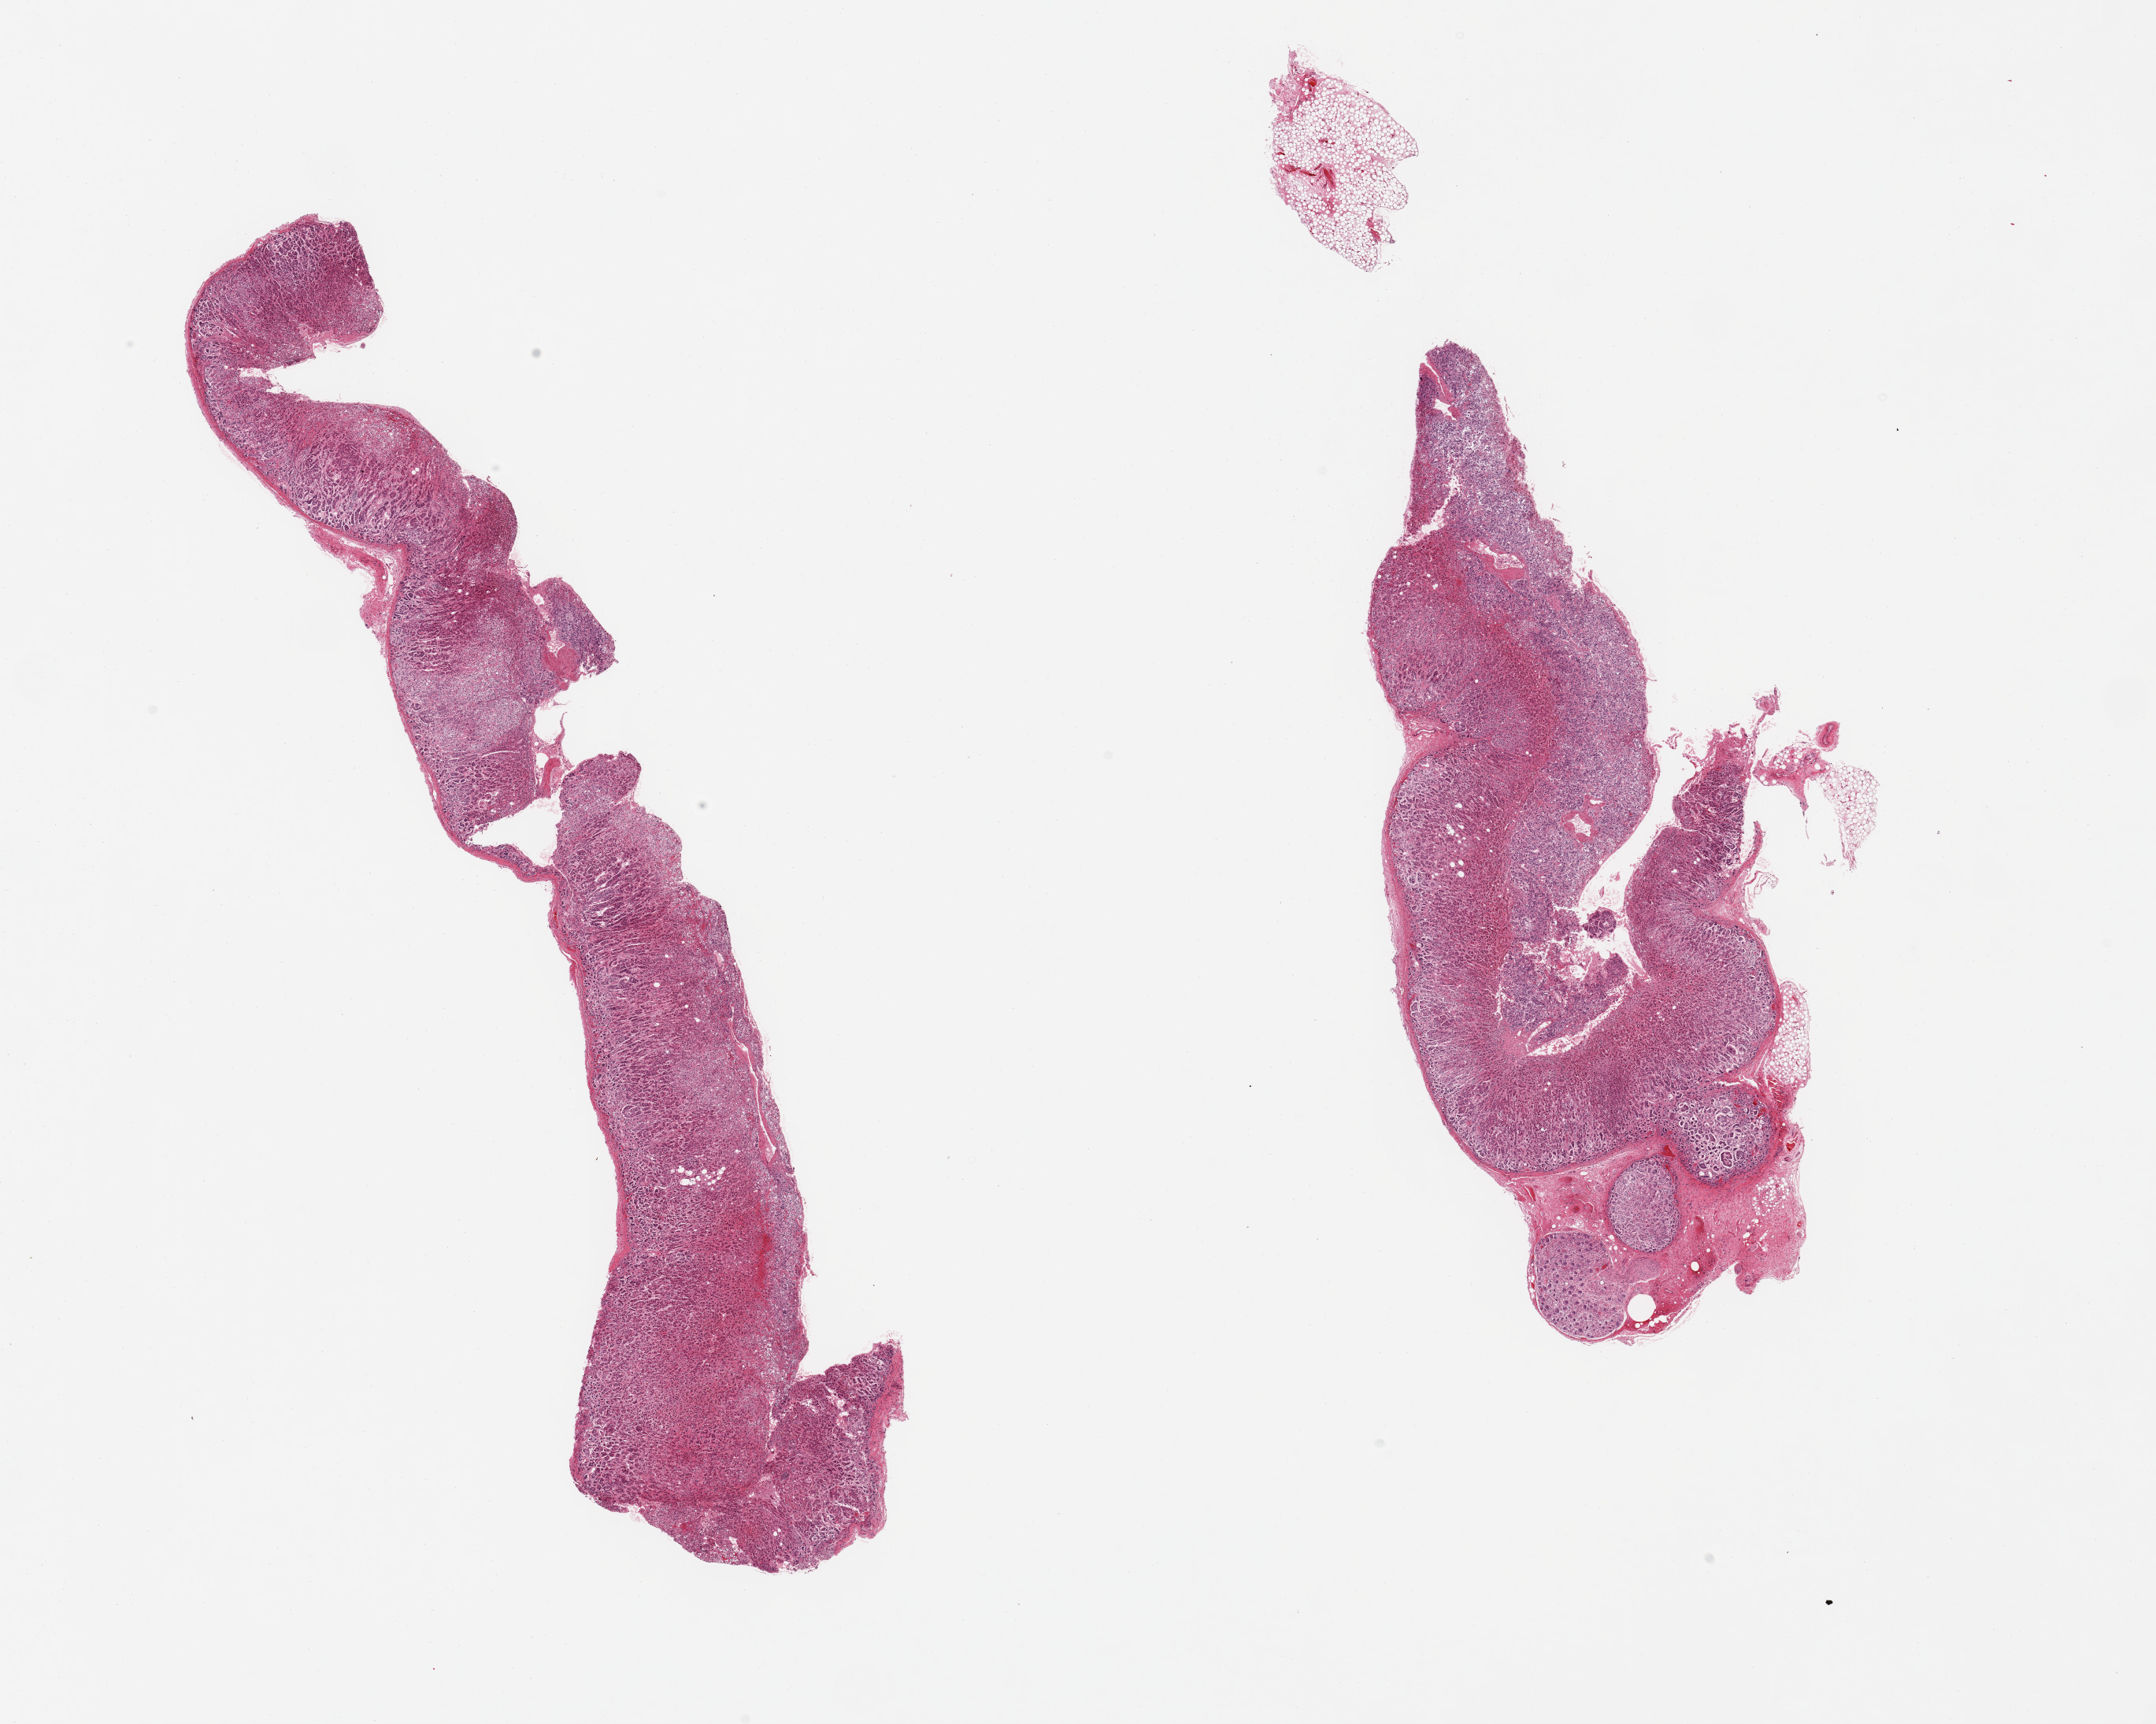
Haematoxylin and eosin whole-slide image, shown as a low-resolution overview of the whole scanned area (about 21.7 x 17.3 mm). PAXgene-fixed, paraffin-embedded tissue. Sampled site (target tissue): adrenal gland. Donor tissue sample. Male donor.
Review note (as recorded): 2 pieces; well trimmed.